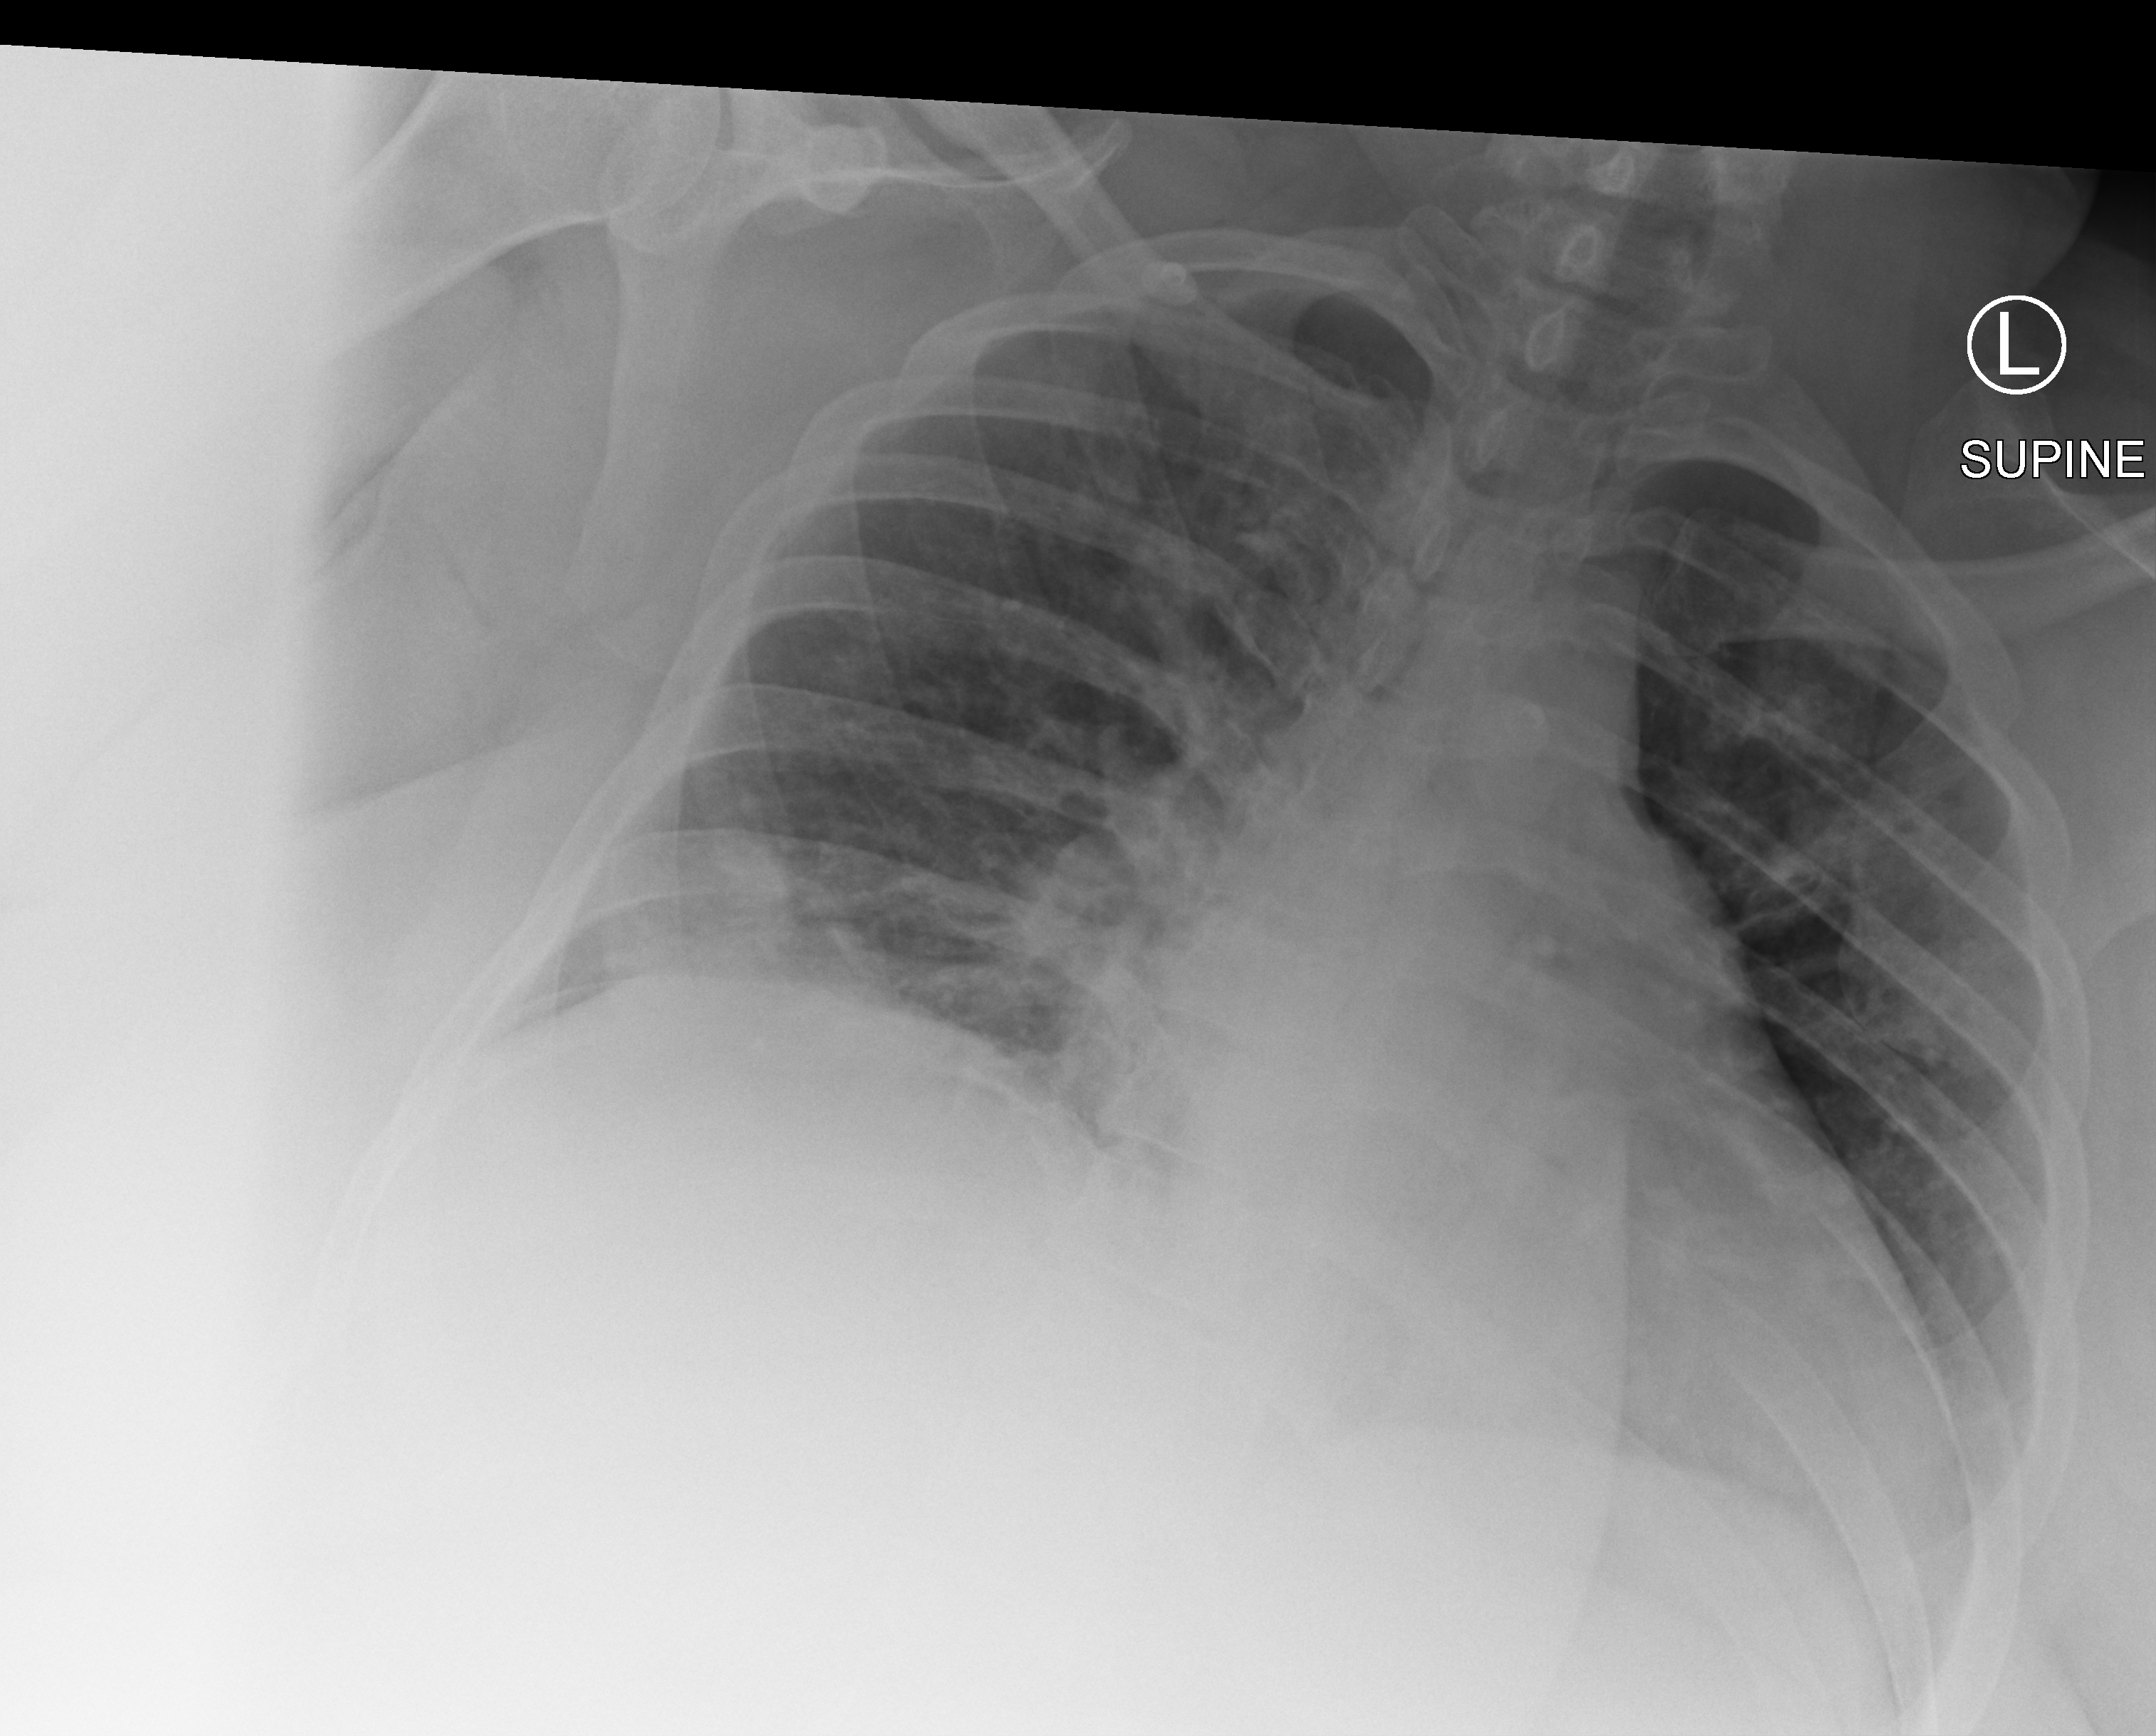
Bedside chest radiograph (computed radiography). Female patient hospitalised with COVID-19, age 18–59 years.
From the hospital-stay record, not from the radiograph (when in the stay this image was taken is not recorded): mechanically ventilated during this hospital stay: no; admitted to intensive care during this hospital stay: no.